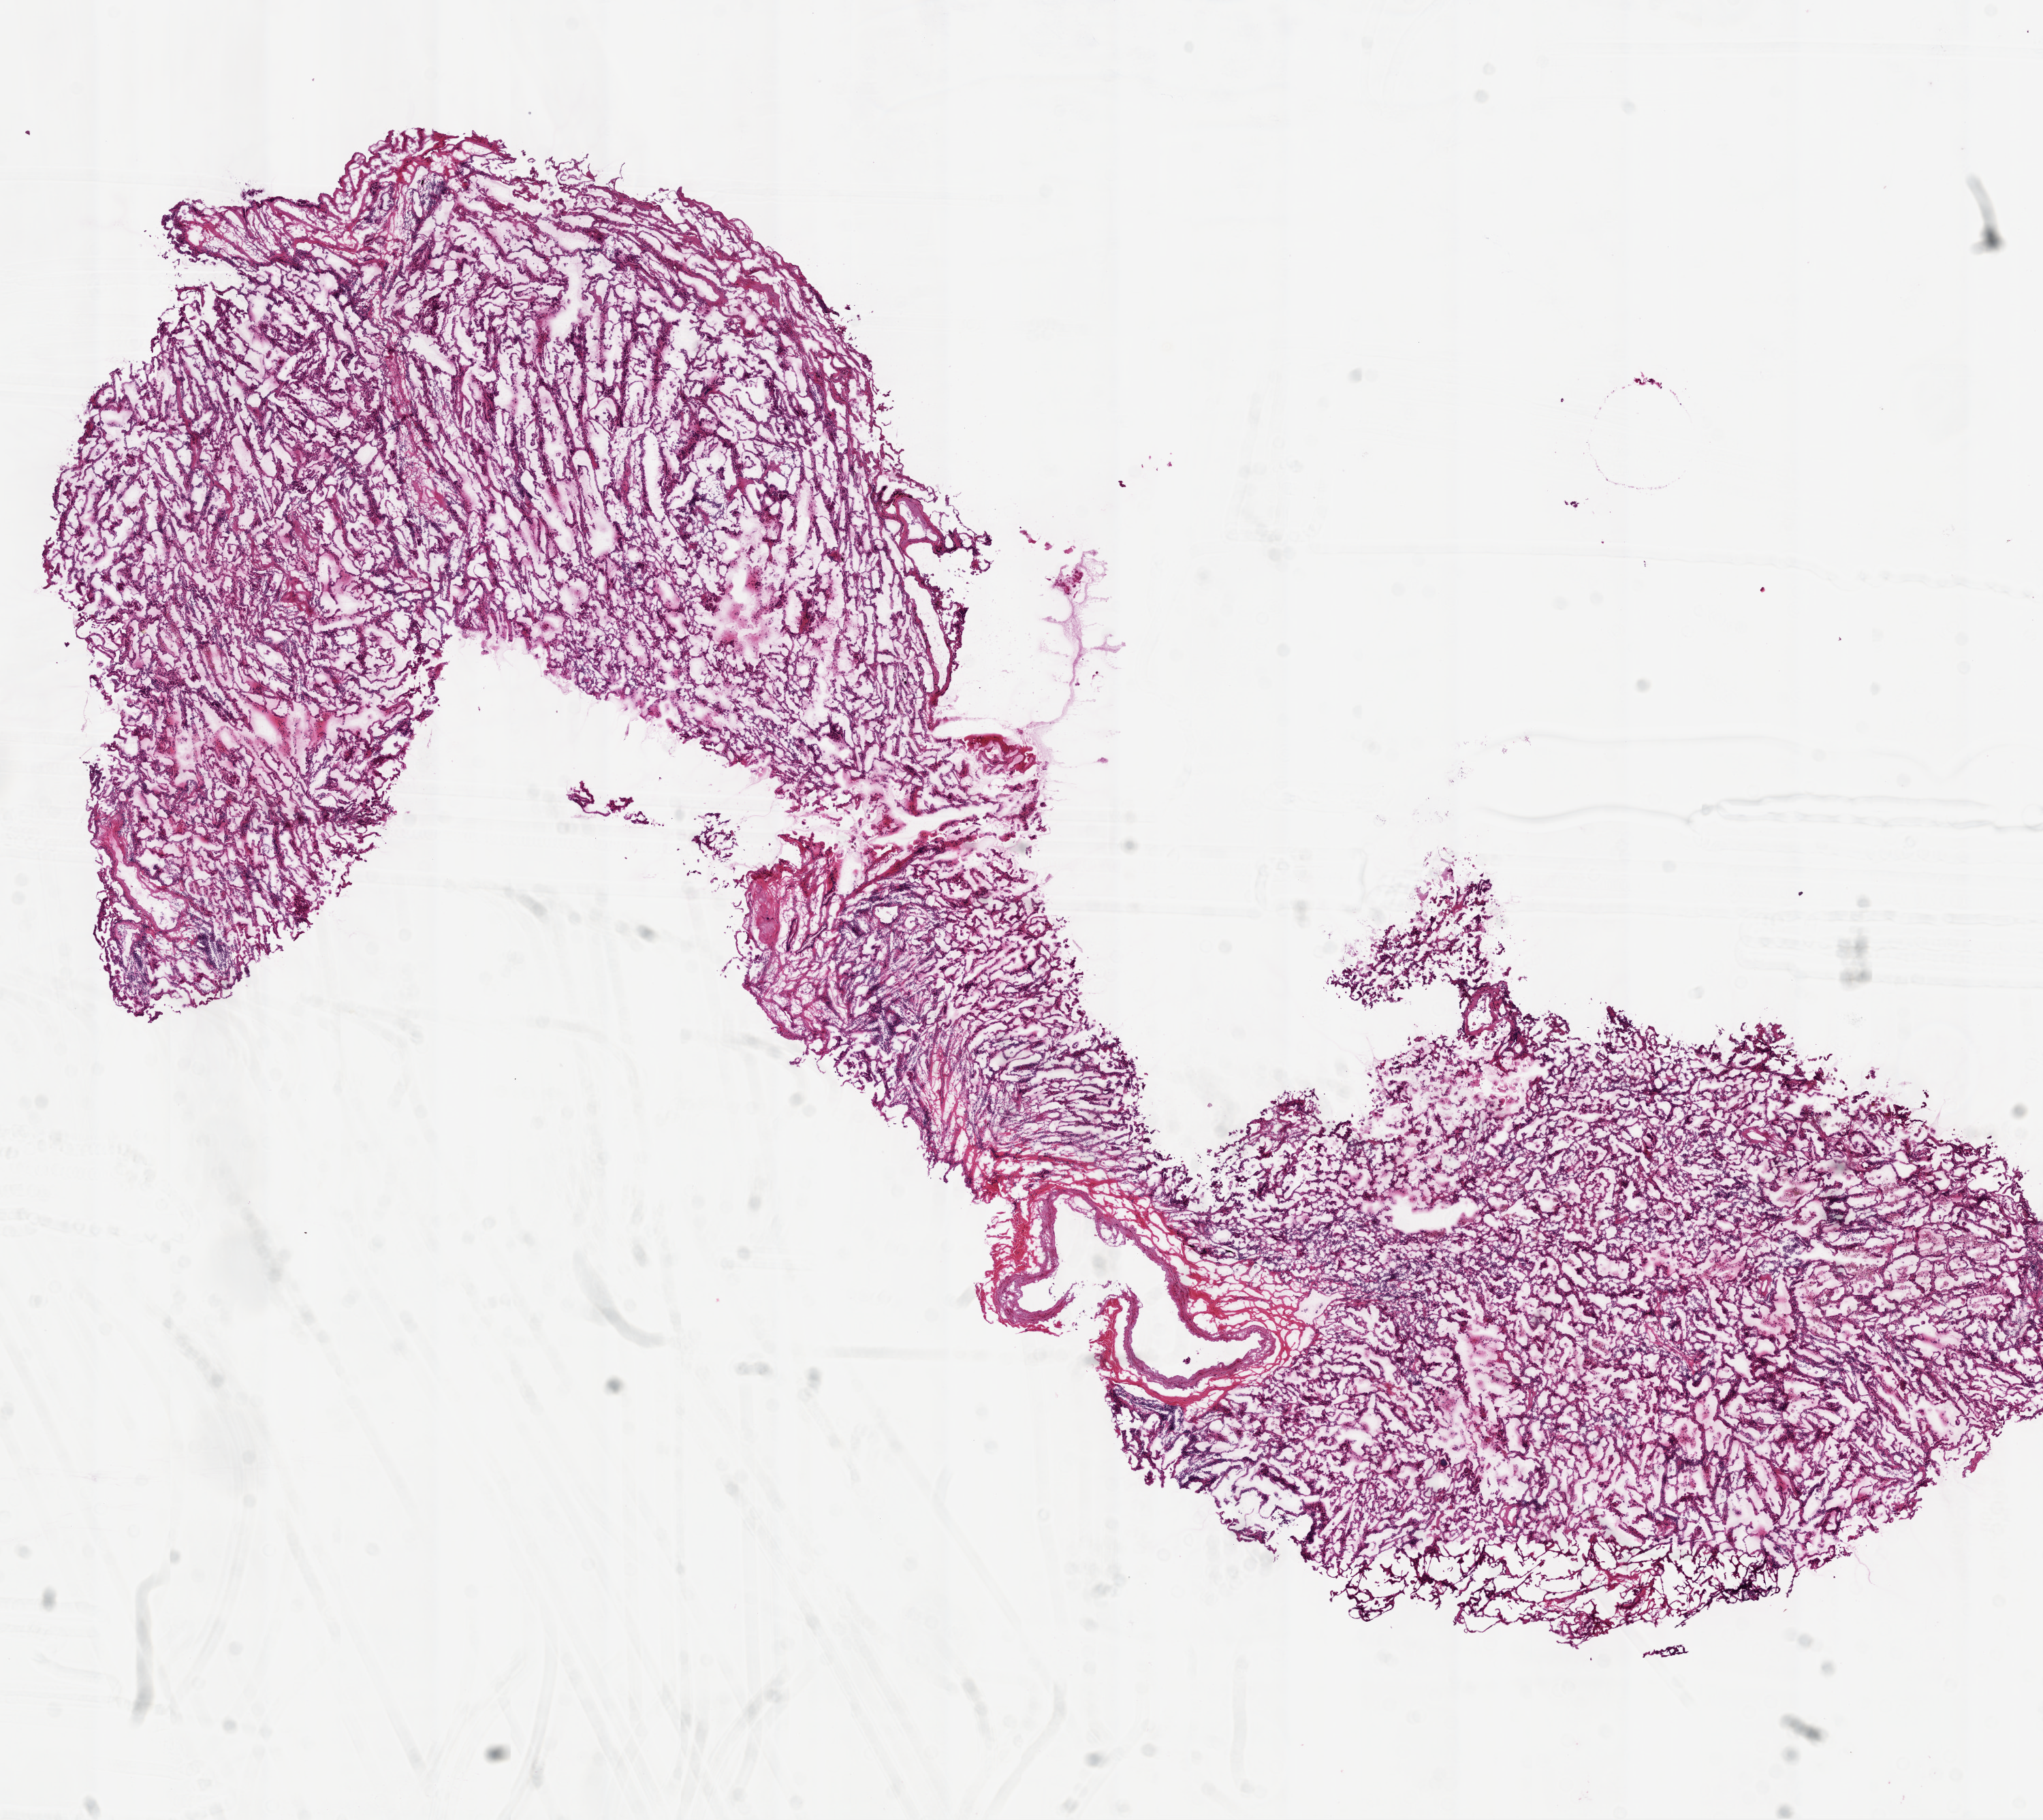
H&E whole-slide image — a low-resolution overview of the entire scanned area, about 12.0 x 10.7 mm (from a 20x scan), frozen section from the top of the tissue portion, primary tumour sample from the lung. Patient: male, age at initial diagnosis 60 years. Composition of this section per pathologist review: tumour cells 90%, tumour nuclei 75%, normal cells 0%, stromal cells 10%, necrosis 0%. Infiltration values recorded for this section: lymphocyte infiltration 10%, monocyte infiltration 5%, neutrophil infiltration 0%.
AJCC pathologic stage: IB (6th edition). Laterality: right. Histologic diagnosis: Bronchiolo-alveolar carcinoma, non-mucinous (upper lobe, lung).